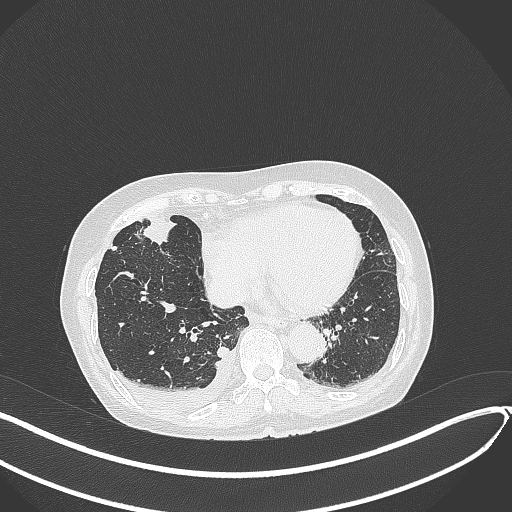
Chest CT, one axial slice. Position 121 of 418 along the scan axis. 120 kVp. Lung window (W 1500 / L -600 HU). 1 mm slice thickness. 512 × 512 image matrix. Female patient, age 75 years. From the clinical record (not read from this slice): clinical TNM (as recorded): T2a N3 M0.
Outlined on this slice (rectangle marked by the reading radiologist):
- lung tumour (recorded histology: adenocarcinoma): bounding box <140,215,178,248> (left, top, right, bottom; pixels)